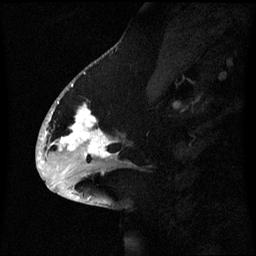
Breast MRI (dynamic contrast-enhanced), one sagittal slice. Slice 27 of 60 in the series (ordered by position). Dynamic contrast-enhanced series, image 2 of 3 at this slice position (ordered by acquisition). 1.5 T. TE 4.2 ms, TR 8.4 ms. 2.1 mm slice thickness. 256 × 256 image matrix. Patient: female, 53 years. Case-level facts recorded for this patient, not image findings: setting: breast cancer imaged before/during neoadjuvant chemotherapy; receptor status: HR-positive, HER2-negative.
Outlined on this slice (semi-automatic segmentation, software-assisted and operator-edited):
- analysis volume of interest (the breast-tissue region the enhancement analysis was run in; not a lesion): box from (x=52, y=90) to (x=131, y=171) px
- tumour enhancement mask (voxels above the 70 % enhancement threshold inside the analysis volume of interest): (x=52, y=102)–(x=113, y=159)